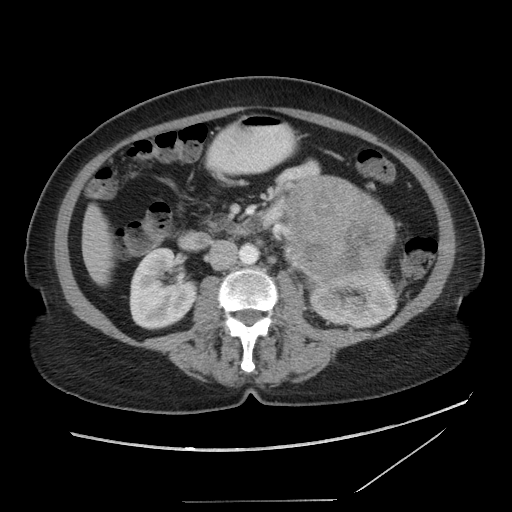
Contrast-enhanced abdominal CT, one axial slice; slice 45 of 86 in the series (ordered by position); intravenous contrast given; soft-tissue window (W 400 / L 40 HU); 5 mm slice thickness; 512 × 512 image matrix, field of view 398 × 398 mm. Female patient, age 77 years. Case-level facts recorded for this patient, not image findings: diagnosis: adrenocortical carcinoma; tumour side: left adrenal; tumour size at pathology: 13.1 cm; Ki-67 index: 10 %; stage (as recorded): 3.
Annotated regions visible in this slice (semi-automatically segmented with operator editing):
- mass: bounding box <289,177,394,284> (left, top, right, bottom; pixels)